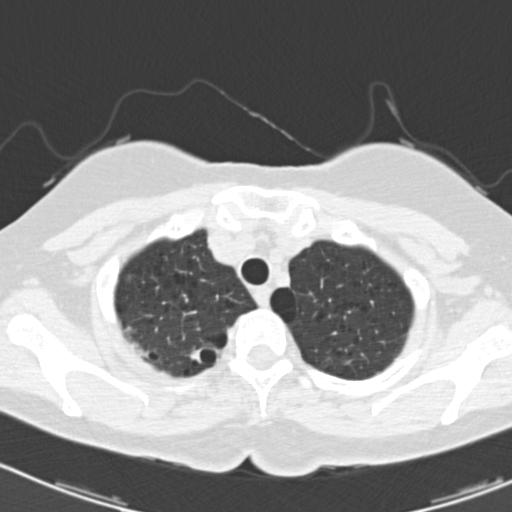
Low-dose screening chest CT, axial slice. Baseline screening round. Lung window (W 1500 / L -600 HU). 2 mm slice thickness. Standard (soft-tissue) reconstruction kernel (B30f). Female, age 64 years at enrolment. Current smoker at enrolment.
Lesion marked by an expert reader, bounding box (x1, y1, x2, y2) in pixels: (179, 335, 224, 375). No non-calcified nodule or mass ≥4 mm was recorded by the screening reader at this exam. Participant outcome: lung cancer diagnosed 402 days after this screen (after the second annual screen) — adenocarcinoma, NOS, right upper lobe, poorly differentiated (G3), stage IB (AJCC 6th edition), 15 mm at pathology.